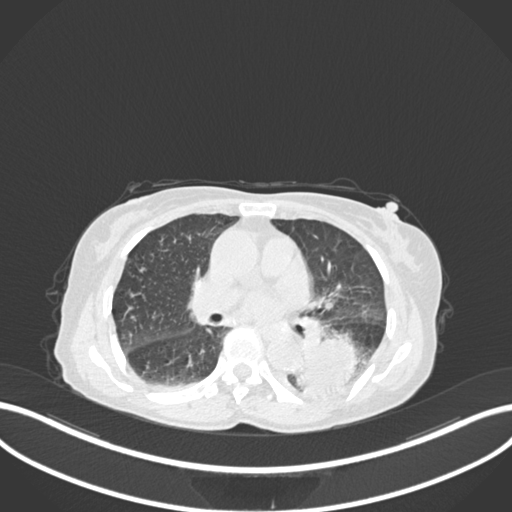
Chest CT, one axial slice; slice 91 of 233 in the series (ordered by position); reconstruction kernel B30f; lung window (W 1500 / L -600 HU); 1 mm slice thickness; 512 × 512 image matrix. Female patient, age 78 years. Case-level facts recorded for this patient, not image findings: clinical TNM (as recorded): T3 N0 M1.
Outlined on this slice (bounding box drawn by a radiologist):
- lung tumour (recorded histology: squamous cell carcinoma): bounding box <295,331,365,401> (left, top, right, bottom; pixels)